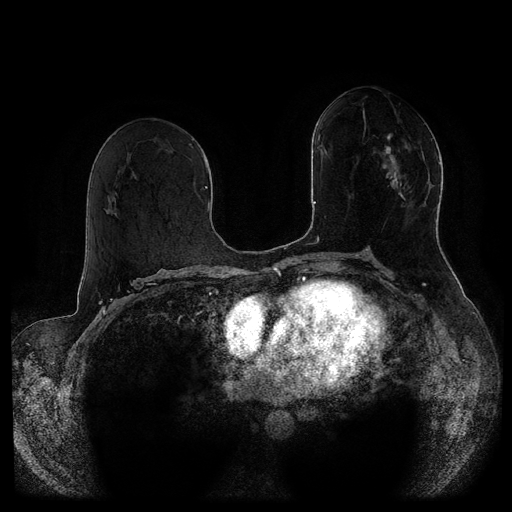
Breast MRI (dynamic contrast-enhanced, multi-phase), one axial slice. Dynamic contrast-enhanced series, time point 2 of 5 at this slice position (early post-contrast). 1.5 T. TE 2.6 ms, TR 5.3 ms. 2 mm slice thickness. 512 × 512 image matrix, field of view 370 × 370 mm. Female patient, age 51 years.
Annotated regions visible in this slice (semi-automatically segmented with operator editing):
- breast lesion (labelled 'tumour' in the annotation; benign lesions carry a separate 'benign' label): bounding box [x1, y1, x2, y2] px = [373, 133, 412, 207]